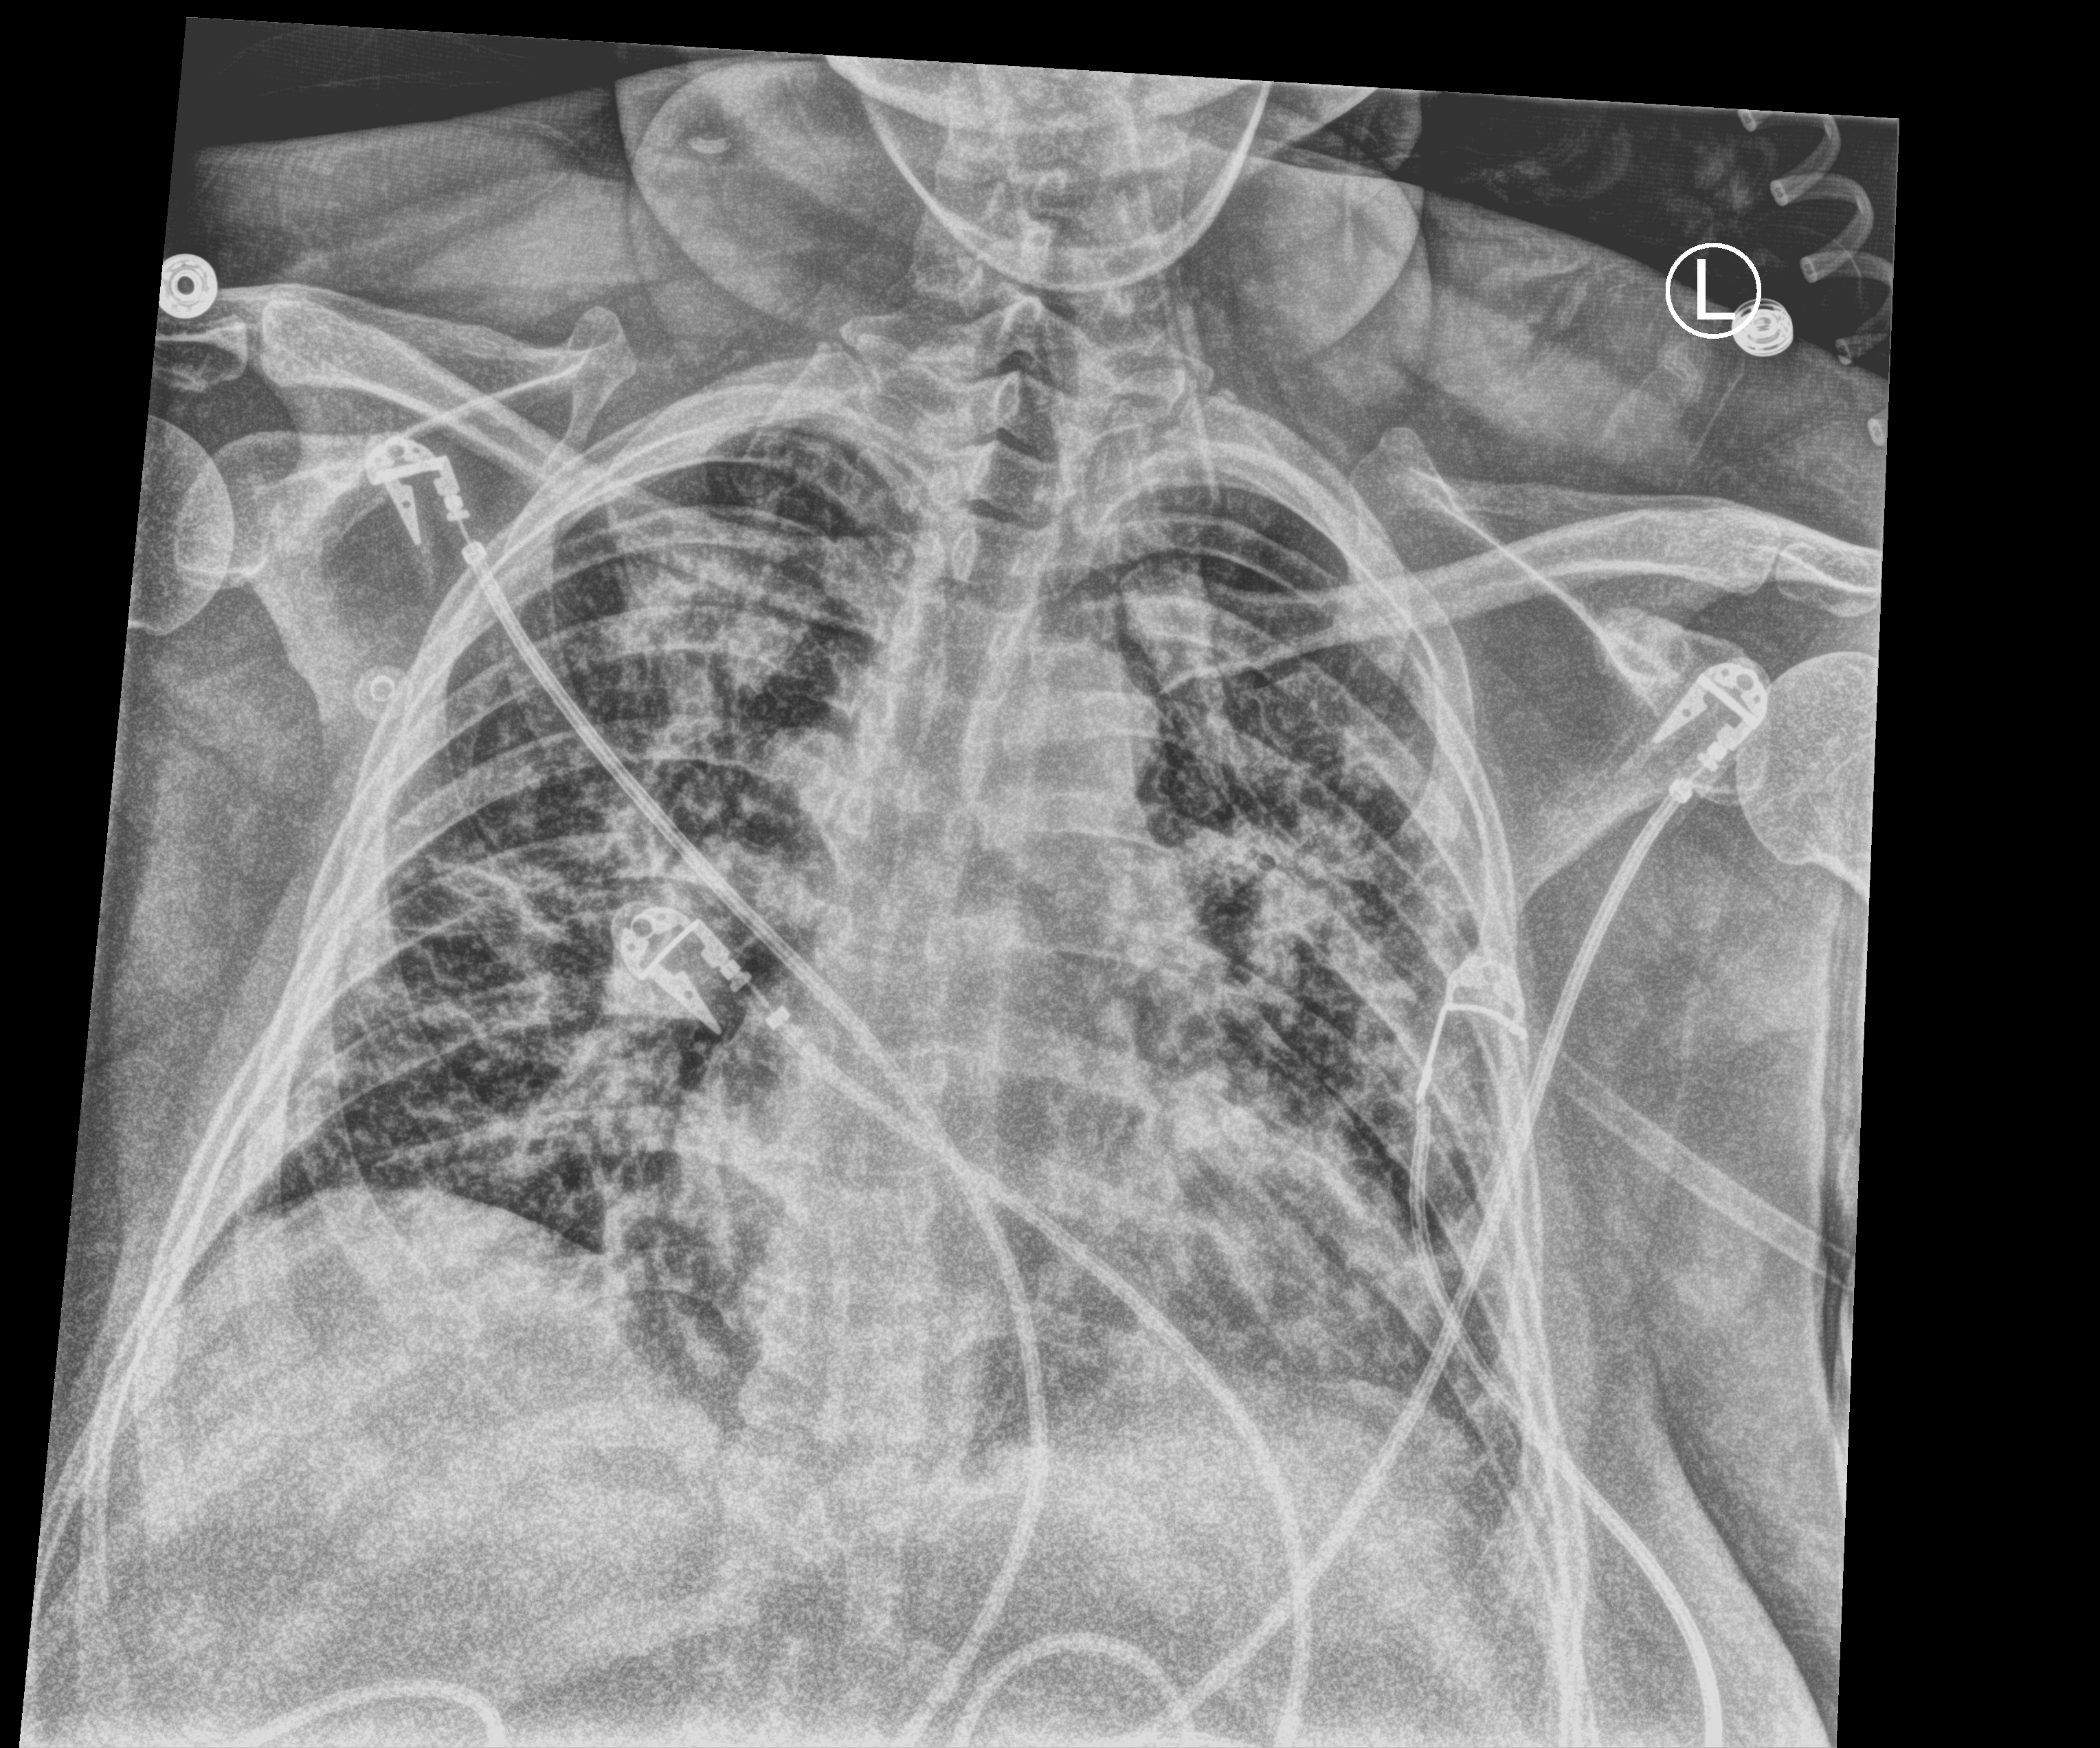
Chest X-ray (portable), anteroposterior (AP) projection. Female patient hospitalised with COVID-19, age 18–59 years.
From the hospital-stay record, not from the radiograph (when in the stay this image was taken is not recorded):
- length of hospital stay: 9 days
- mechanically ventilated during this hospital stay: yes